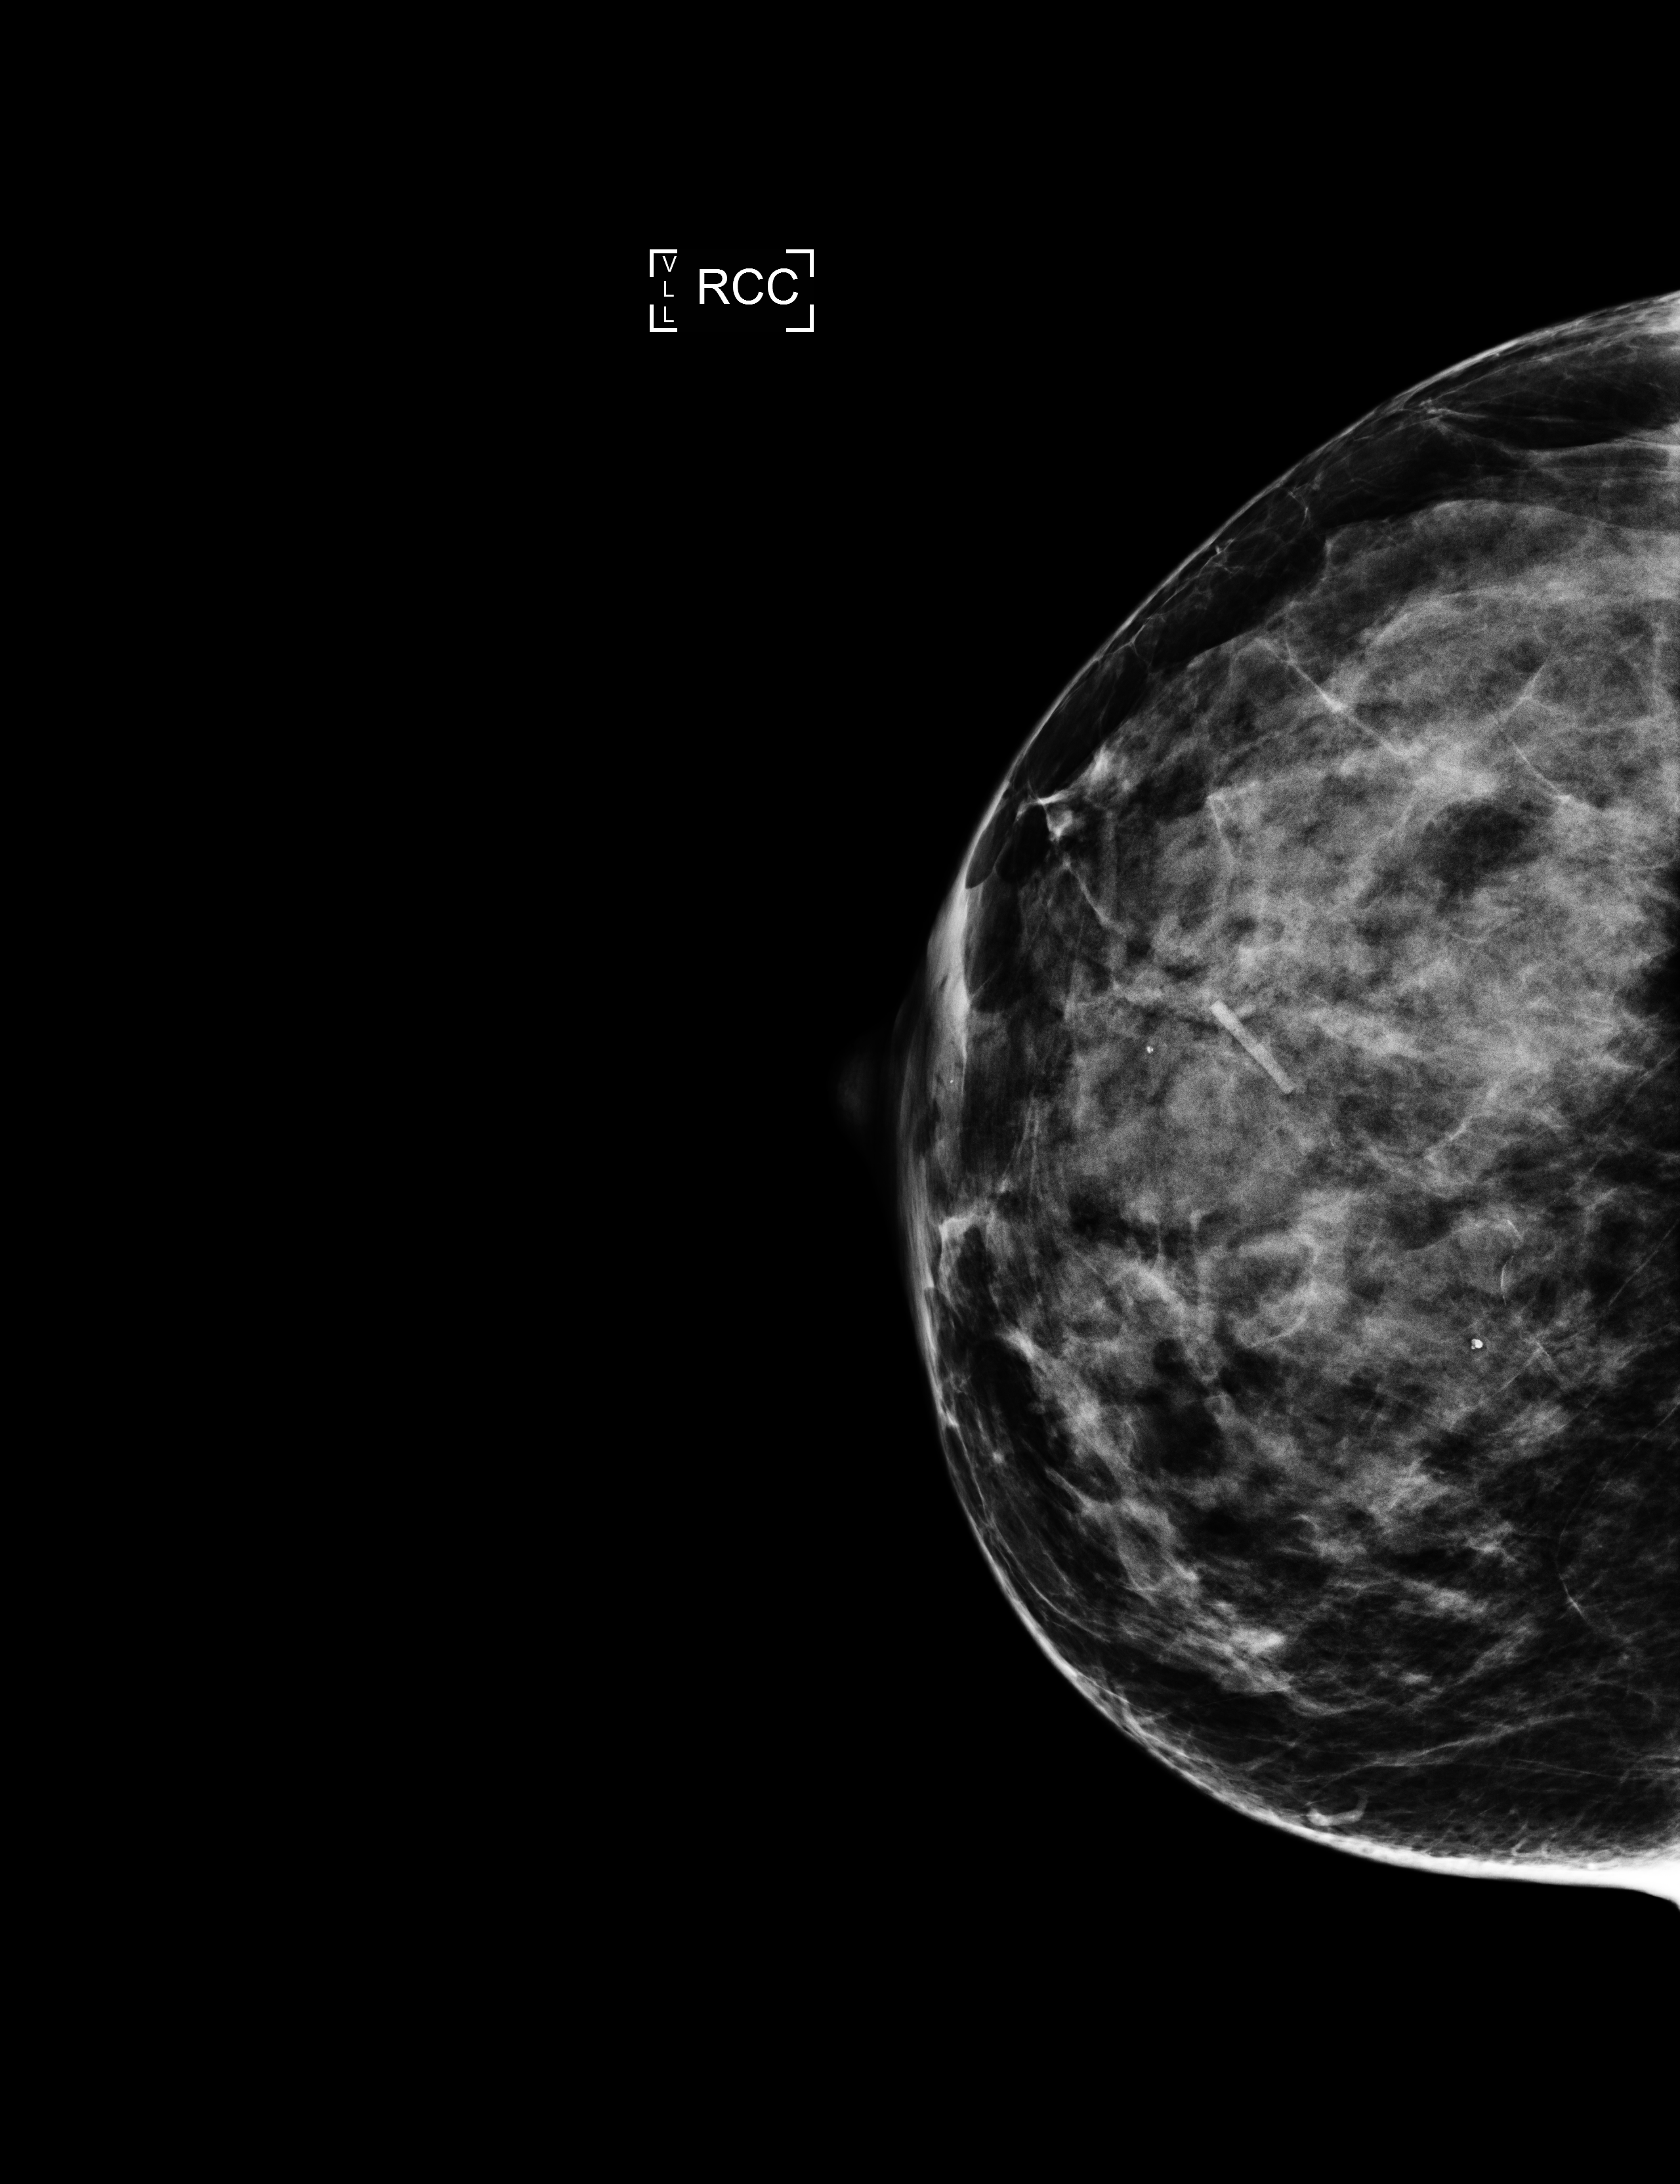
Screening examination. Patient: female, 48 years.
Image type: full-field digital mammogram. Breast: right. Projection: cranio-caudal projection.